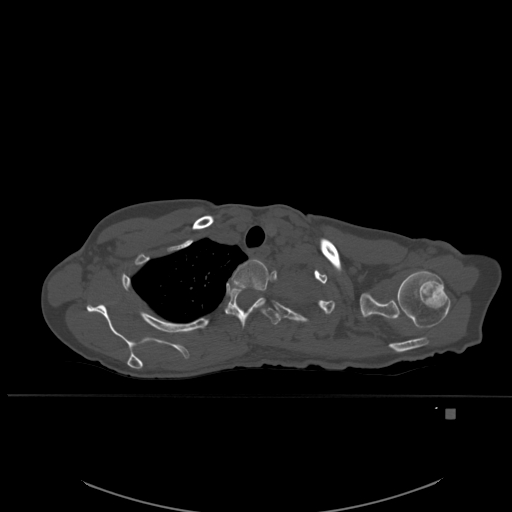
CT including the spine, one axial slice. Position 429 of 537 along the scan axis. Bone window (W 1800 / L 400 HU). 1.5 mm slice thickness. 512 × 512 image matrix. Female patient, age 45 years. From the clinical record (not read from this slice): primary cancer: lung.
Annotated regions visible in this slice (semi-automatic segmentation, software-assisted and operator-edited):
- T2 vertebra: box from (x=232, y=258) to (x=271, y=291) px
- T3 vertebra: (x=225, y=285)–(x=281, y=330)